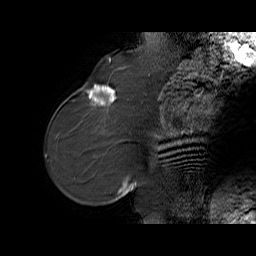
Breast MRI (dynamic contrast-enhanced), one sagittal slice; position 21 of 65 along the scan axis; dynamic contrast-enhanced series, time point 2 of 6 at this slice position (early post-contrast); 1.5 T; TE 5.7 ms, TR 32.9 ms; 4 mm slice thickness; 256 × 256 image matrix. Female patient. From the clinical record (not read from this slice): setting: breast cancer imaged before/during neoadjuvant chemotherapy; receptor status: HER2-positive.
Annotated regions visible in this slice (semi-automatic segmentation, software-assisted and operator-edited):
- analysis volume of interest (the breast-tissue region the enhancement analysis was run in; not a lesion): bounding box [x1, y1, x2, y2] px = [76, 77, 125, 128]
- tumour enhancement mask (voxels above the 100 % enhancement threshold inside the analysis volume of interest): [87, 84, 116, 106]